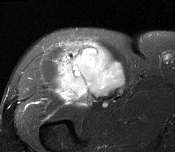
MRI of an extremity soft-tissue mass, one axial slice. Position 105 of 116 along the scan axis. T2-weighted fat-saturated. MR volume resampled by the dataset authors to the PET/CT grid (not the native acquisition matrix). 3.27 mm slice thickness. 175 × 152 image matrix. Male patient. Case-level facts recorded for this patient, not image findings: histological type: pleiomorphic leiomyosarcoma; grade: intermediate; site of the primary tumour: right thigh.
Annotated regions visible in this slice (expert contour drawn on MRI and transferred to this co-registered scan by the dataset authors):
- gross tumour volume including surrounding oedema: box from (x=56, y=42) to (x=125, y=101) px
- gross tumour volume (mass): (x=58, y=47)–(x=125, y=100)